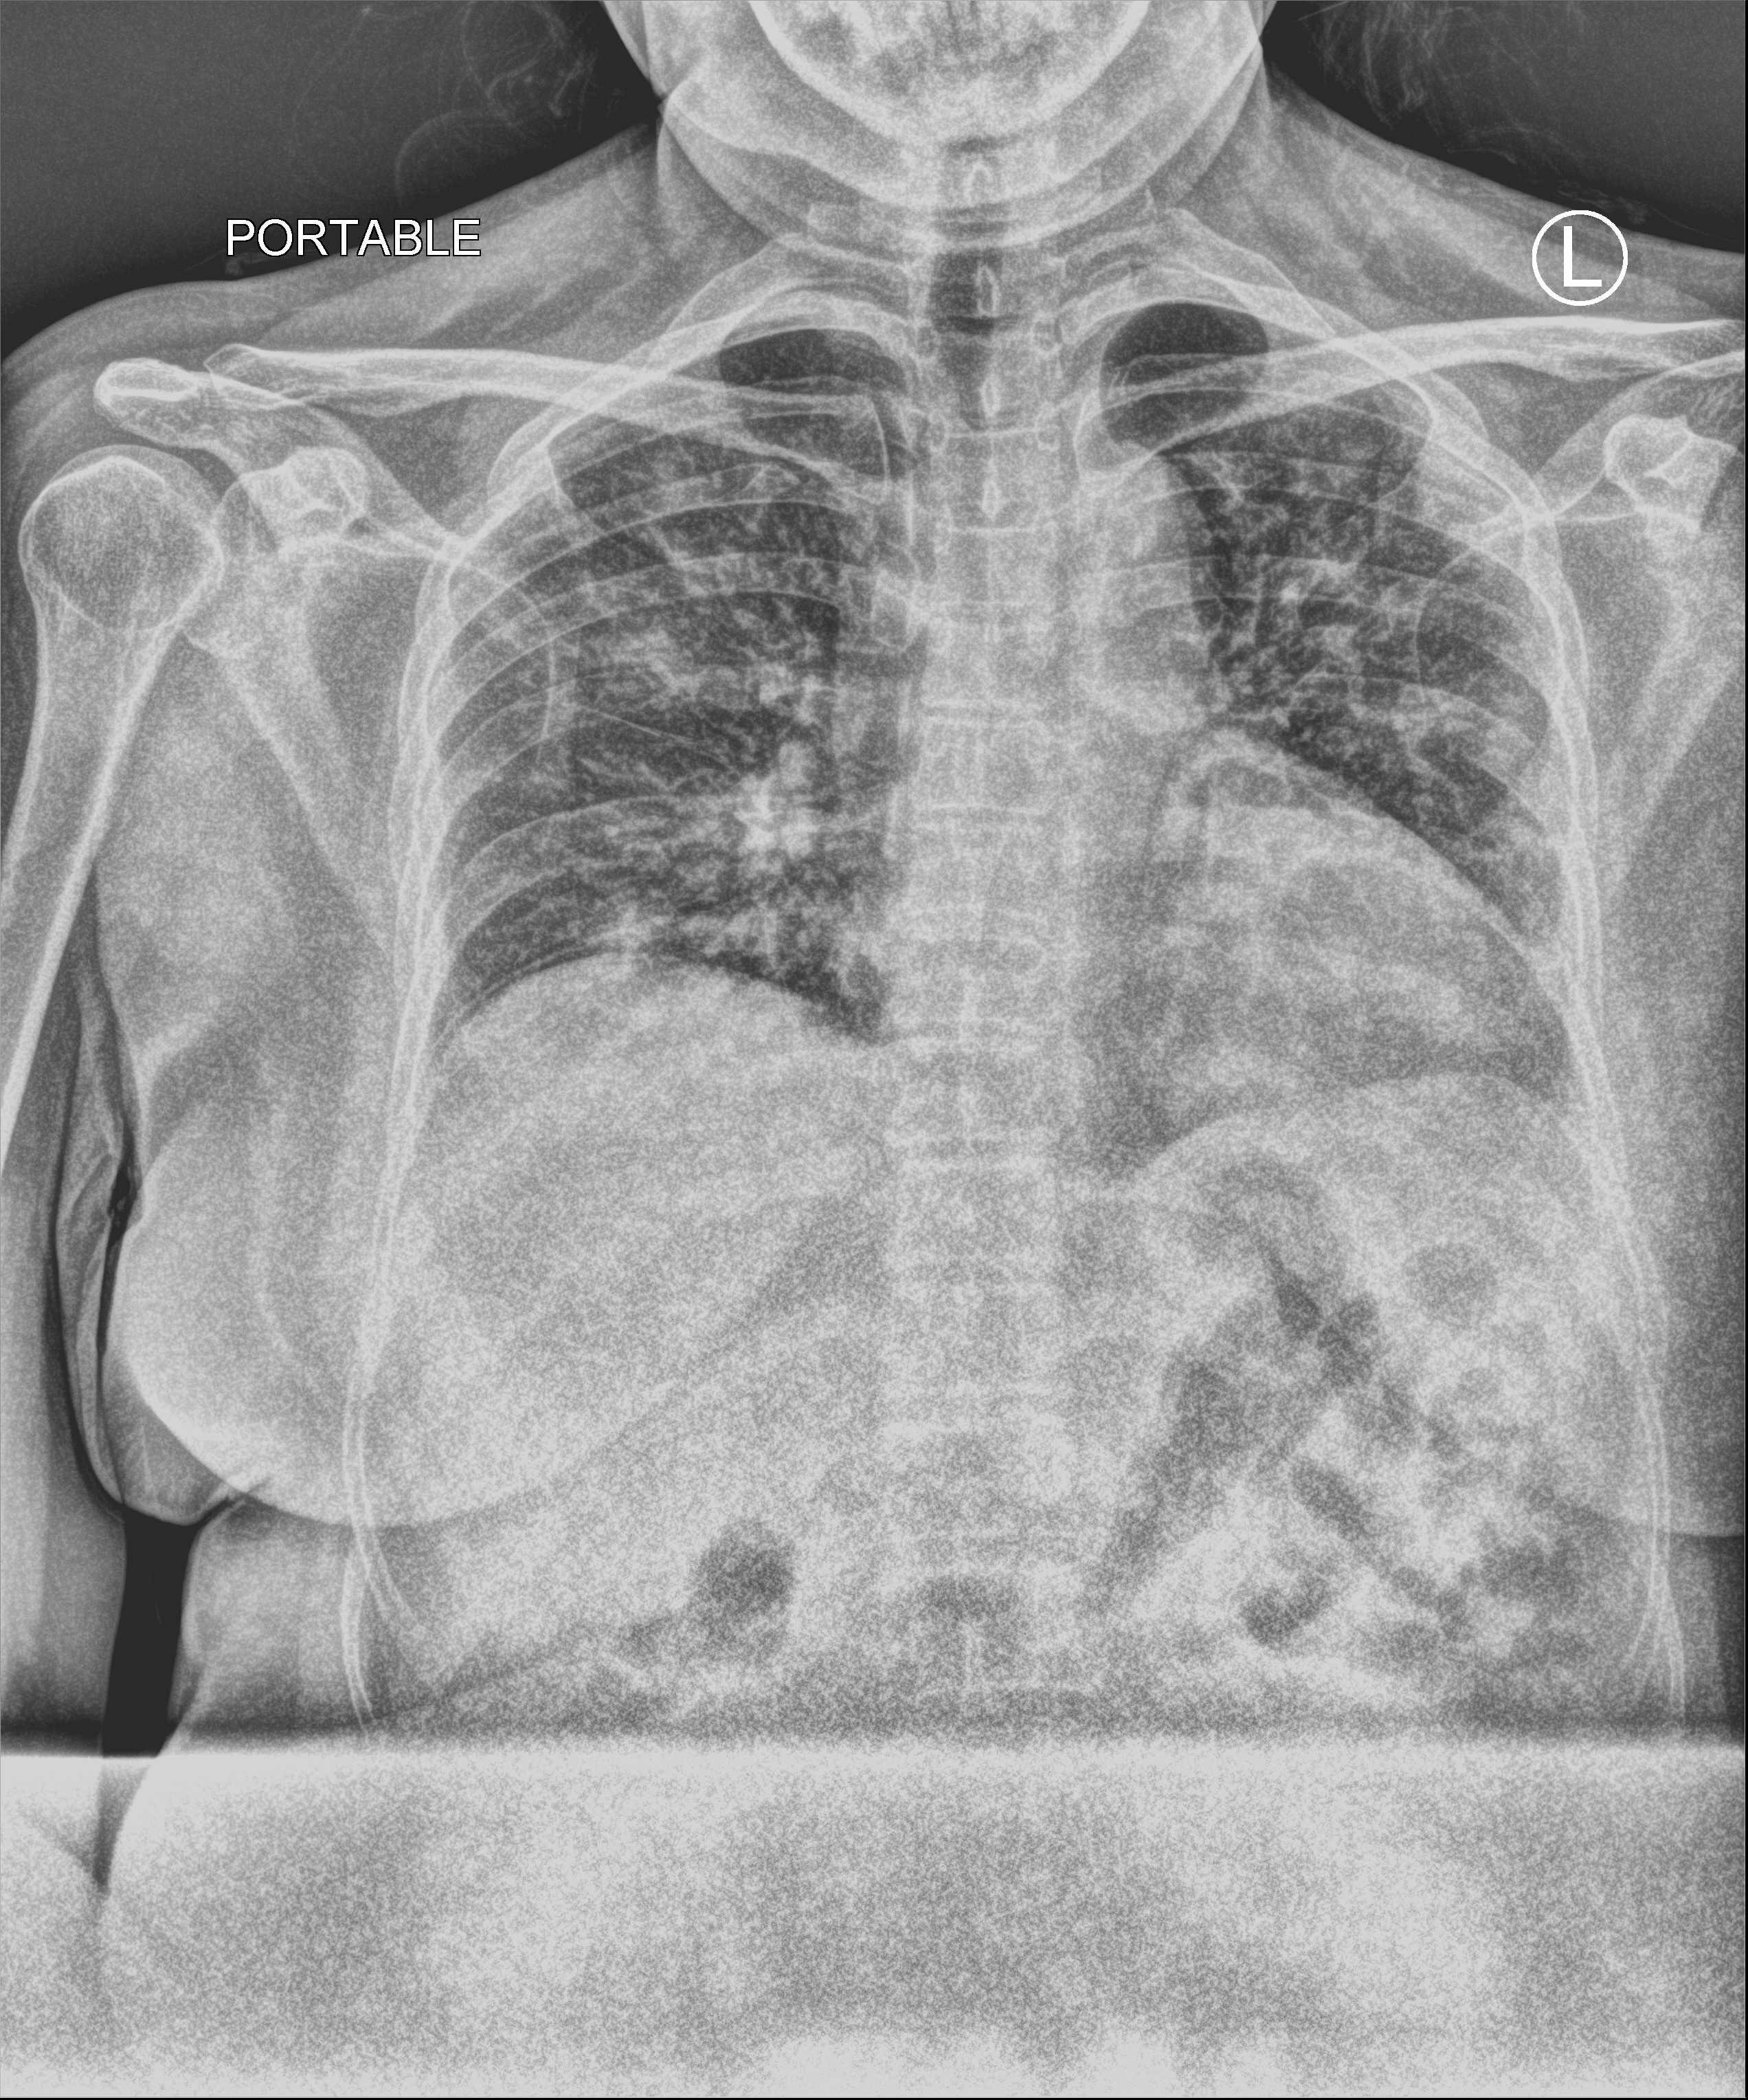
Portable chest radiograph; anteroposterior (AP) projection. Patient hospitalised with COVID-19; female, aged 18–59 years.
Admission-level facts for this patient (not findings on this image; timing relative to this image not recorded):
- mechanically ventilated during this hospital stay: no